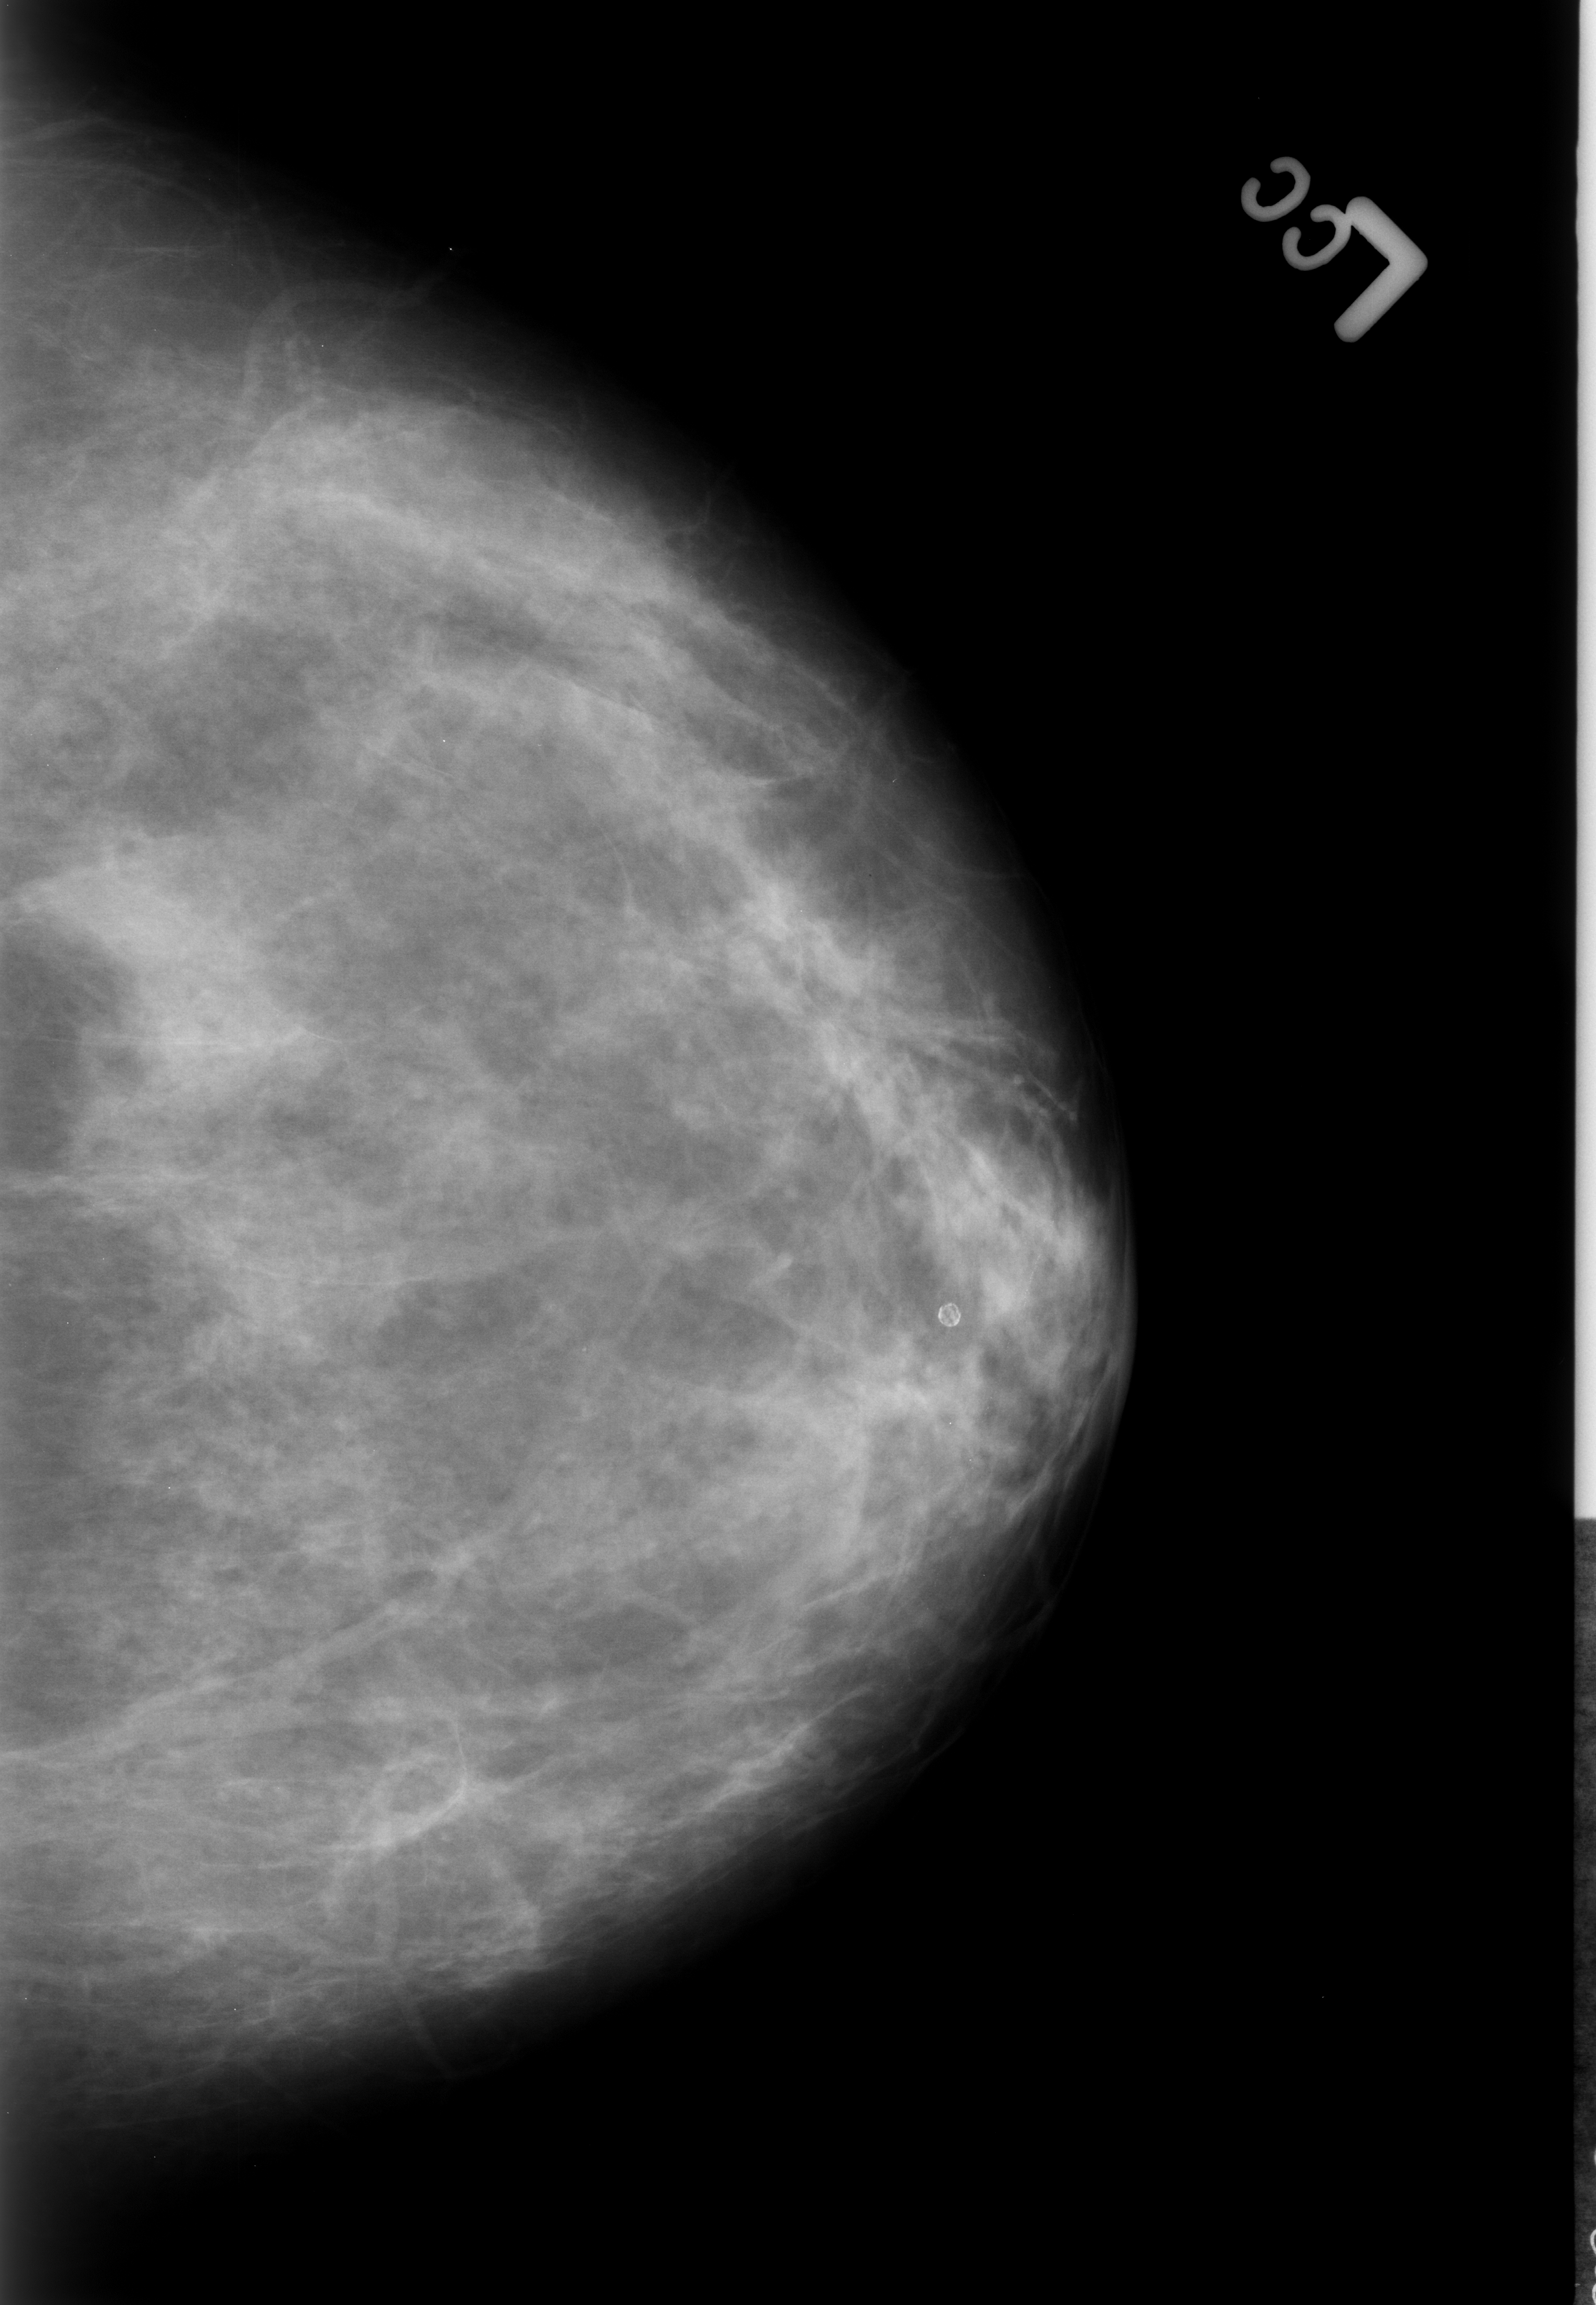
Digitized screen-film mammogram; left breast; CC view; BI-RADS breast density category 2 (scale 1–4).
- Finding: calcifications, morphology lucent center; BI-RADS assessment category 2; benign without callback (not worked up further).